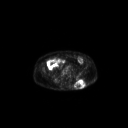
FDG PET of an extremity soft-tissue mass (from a PET/CT study), one axial slice. Slice 84 of 267 in the series (ordered by position). 3.27 mm slice thickness. 128 × 128 image matrix, field of view 700 × 700 mm. Patient: male, 69 years. Case-level facts recorded for this patient, not image findings: histological type: leiomyosarcoma; grade: intermediate; site of the primary tumour: left pelvis.
Outlined on this slice (expert contour drawn on MRI and transferred to this co-registered scan by the dataset authors):
- gross tumour volume (mass): bounding box [x1, y1, x2, y2] px = [74, 78, 86, 89]